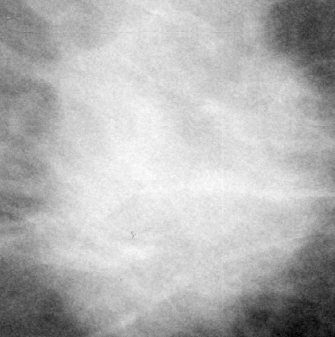
Crop from a digitized film mammogram around one marked abnormality, left breast, MLO view.
Mass, shape round, margins spiculated; BI-RADS assessment category 4; pathology result (as recorded, not read from the image): malignant.